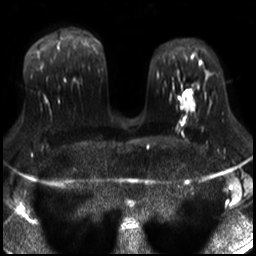
Breast MRI, one axial slice; position 17 of 30 along the scan axis; diffusion-weighted series; image 2 of 4 stored at this slice position (different b-values; order by instance number); 3 T; 4 mm slice thickness; 256 × 256 image matrix, field of view 320 × 320 mm. Female patient.
Outlined on this slice (expert manual segmentation):
- tumour on diffusion-weighted imaging: bounding box (x1, y1, x2, y2) in pixels: (181, 95, 194, 111)